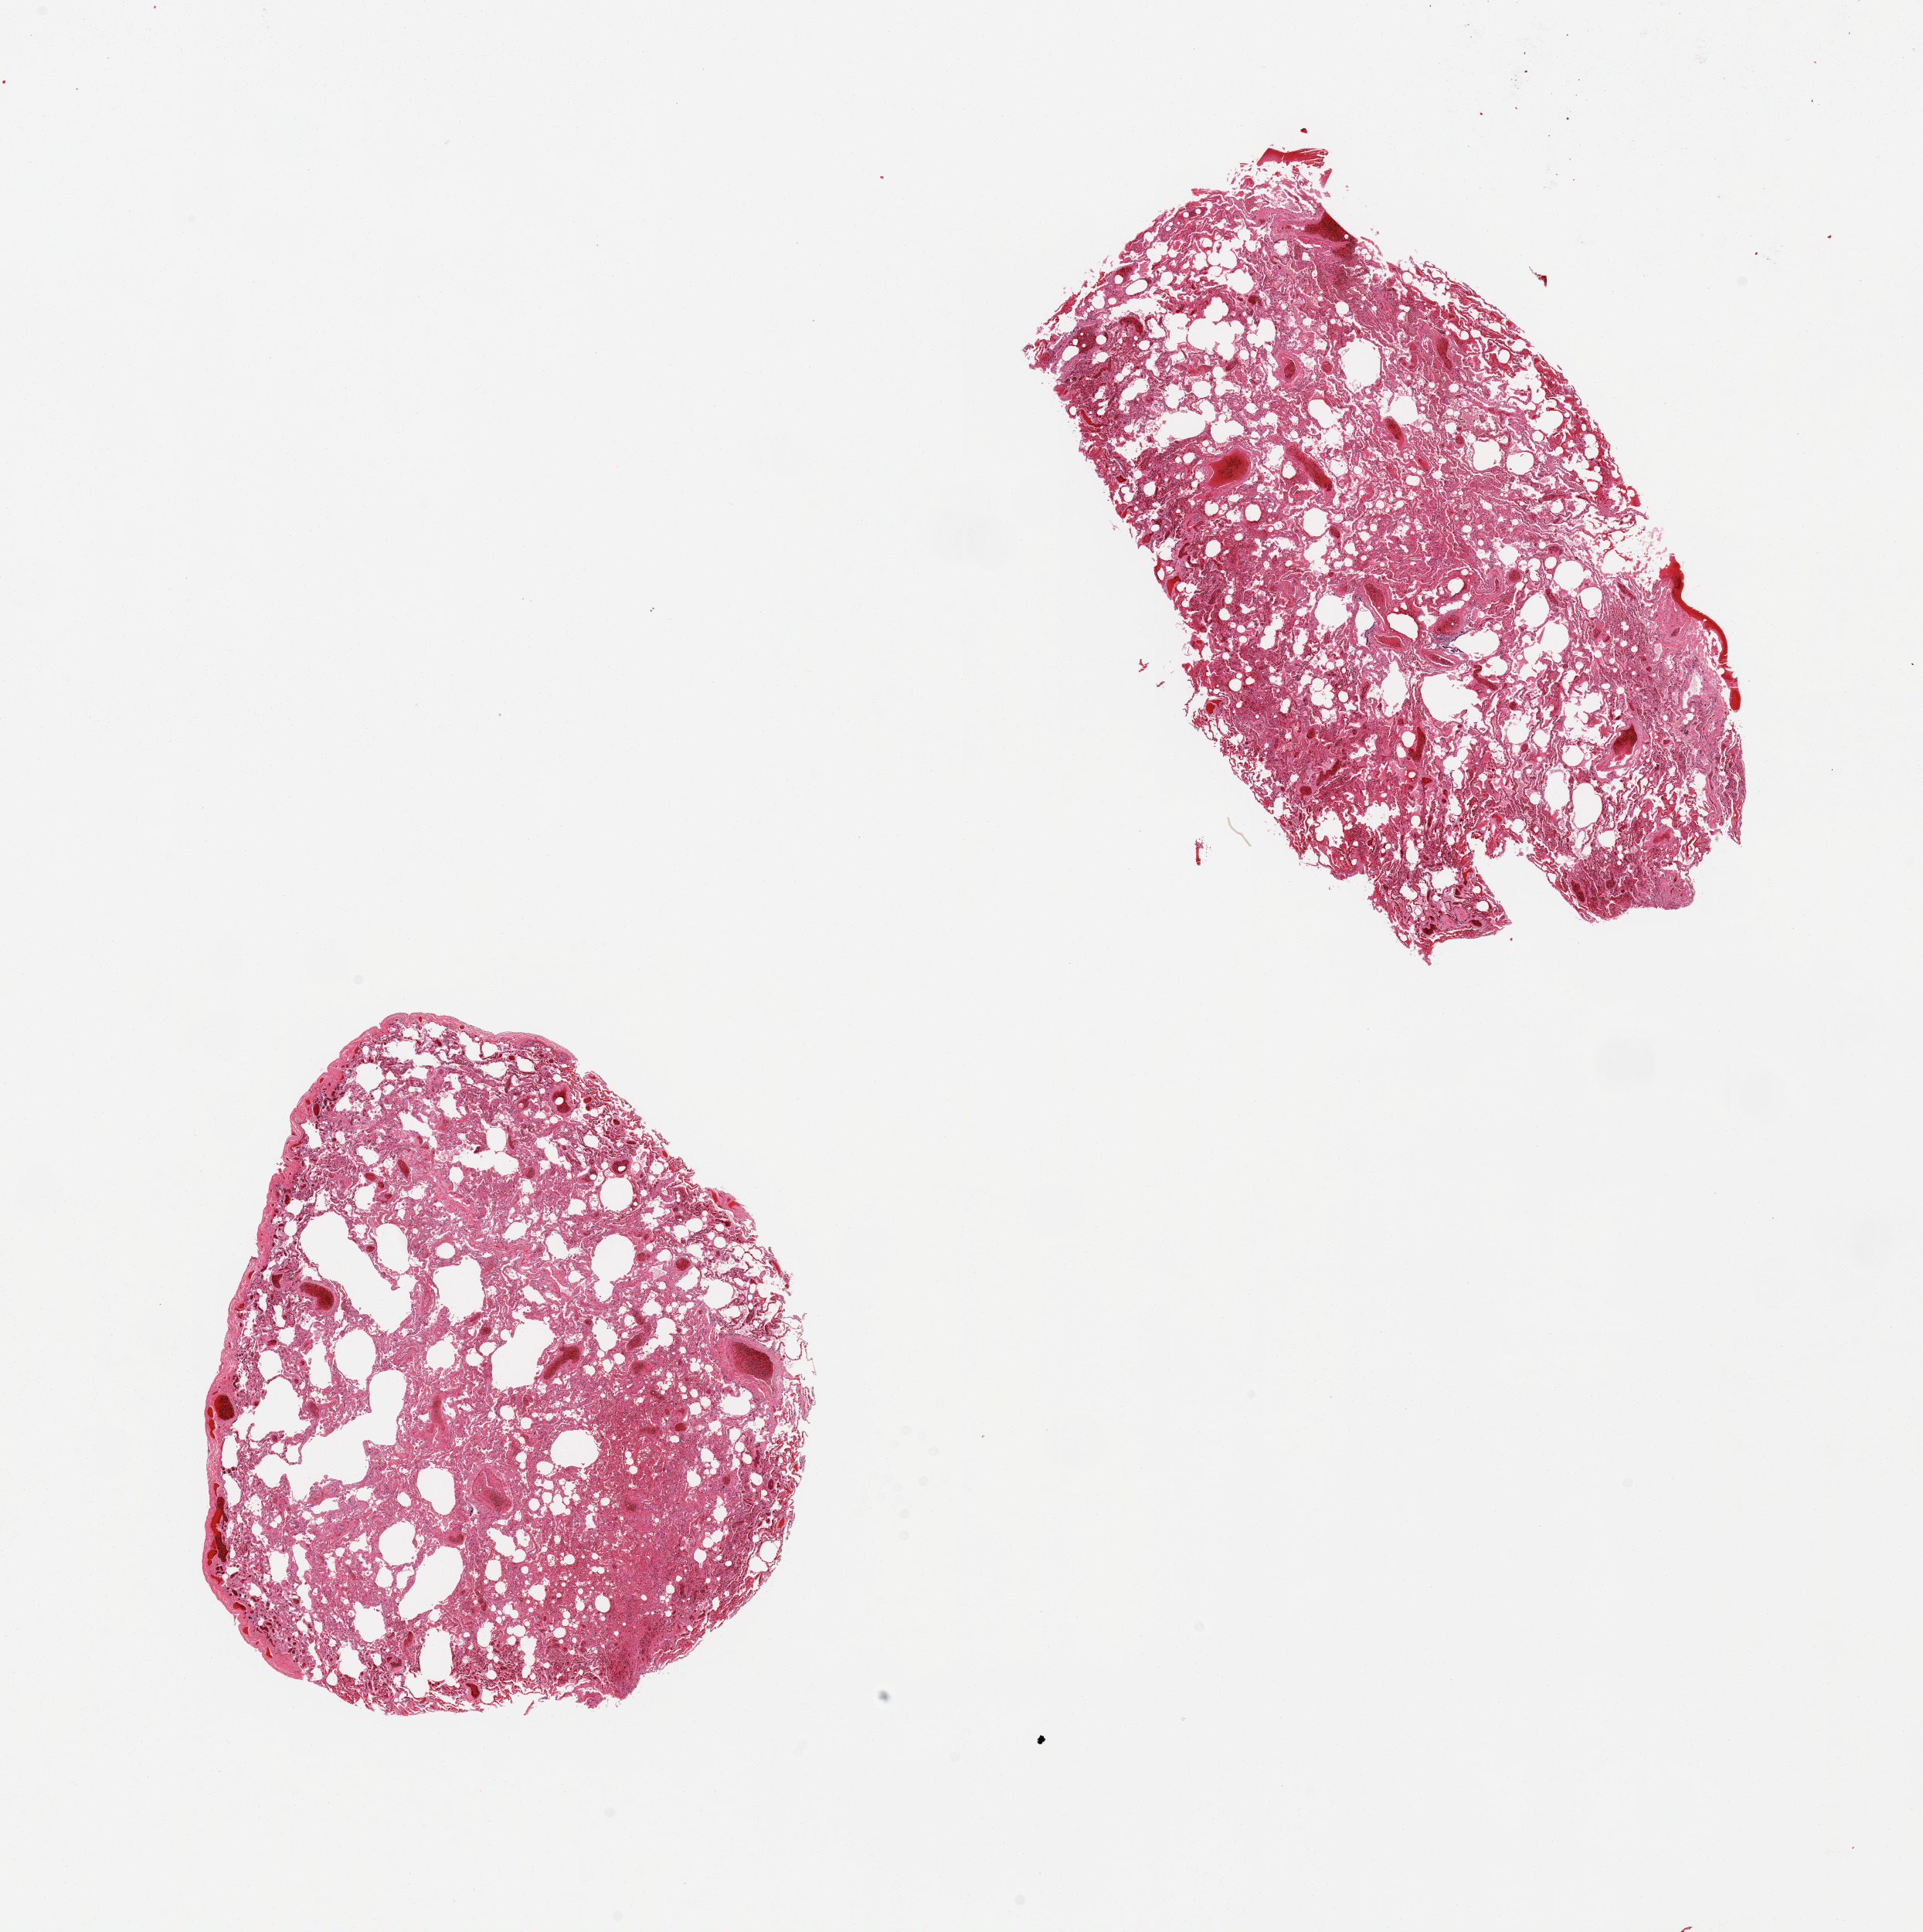
Hematoxylin and eosin (H&E) whole-slide image — shown as a low-resolution overview of the whole scanned area (about 19.7 x 19.8 mm, slide scanned at 20x), PAXgene-fixed, paraffin-embedded tissue, sampled site (target tissue): lung, tissue donor sample.
Pathologist's review note for this sample: 2 pieces; emphysema.